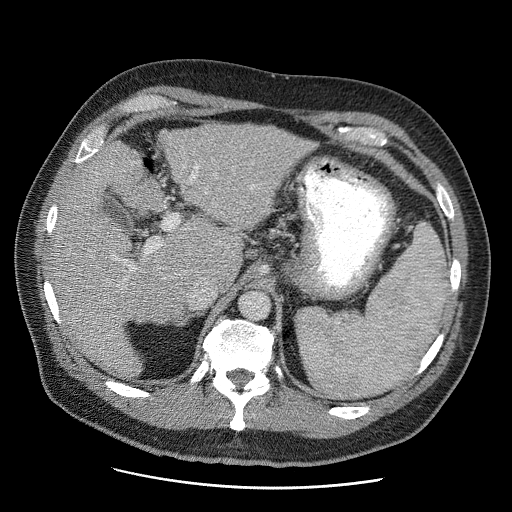
Contrast-enhanced abdominal CT (liver protocol), one axial slice; slice 34 of 81 in the series (ordered by position); 120 kVp; soft-tissue window (W 400 / L 40 HU); 512 × 512 image matrix, field of view 380 × 380 mm. From the clinical record (not read from this slice): diagnosis: hepatocellular carcinoma (patient treated with transarterial chemoembolisation; whether this scan precedes or follows treatment is not stated here); TNM stage (as recorded): Stage-IIIA; Child-Pugh class: A; tumour differentiation: moderately differentiated.
Annotated regions visible in this slice (semi-automatically segmented with operator editing):
- liver parenchyma outside the tumour (the mass and vessels are separate outlines, so this box may not span the whole liver): box from (x=50, y=122) to (x=314, y=376) px
- liver vessels: (x=115, y=166)–(x=252, y=300)